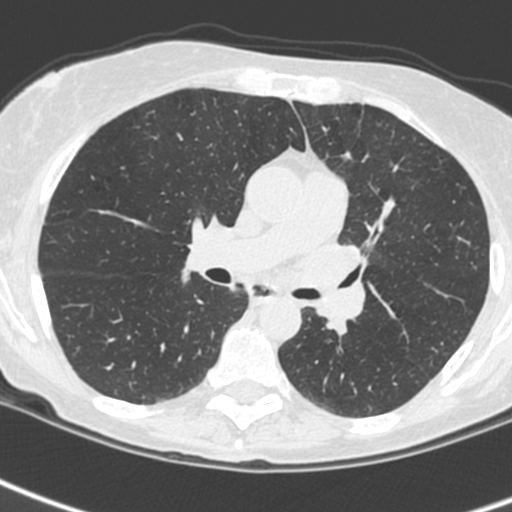
Low-dose screening chest CT, one axial slice; position 144 of 242 along the scan axis; 120 kVp; lung window (W 1500 / L -600 HU); 1.3 mm slice thickness; 512 × 512 image matrix.
Annotated regions visible in this slice (outlined manually by an expert reader):
- lesion 3 (tumor, upper lobe of left lung): box from (x=295, y=239) to (x=368, y=326) px